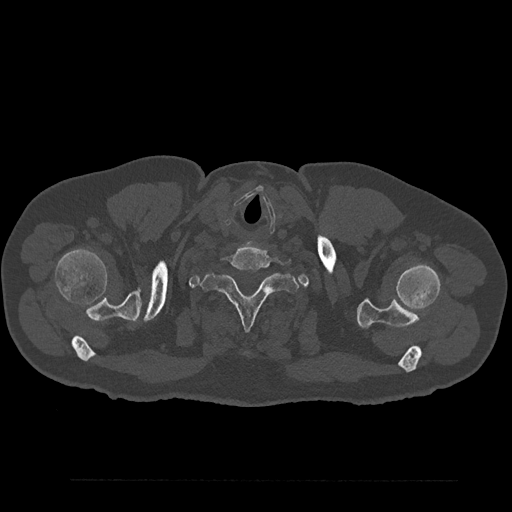
CT including the spine, one axial slice; position 757 of 797 along the scan axis; bone window (W 1800 / L 400 HU); 0.5 mm slice thickness; 512 × 512 image matrix, field of view 430 × 430 mm. Patient: male, 61 years. From the clinical record (not read from this slice): primary cancer: prostate.
Annotated regions visible in this slice (semi-automatically segmented with operator editing):
- T1 vertebra: box from (x=200, y=262) to (x=299, y=331) px
- T2 vertebra: (x=207, y=308)–(x=208, y=312)